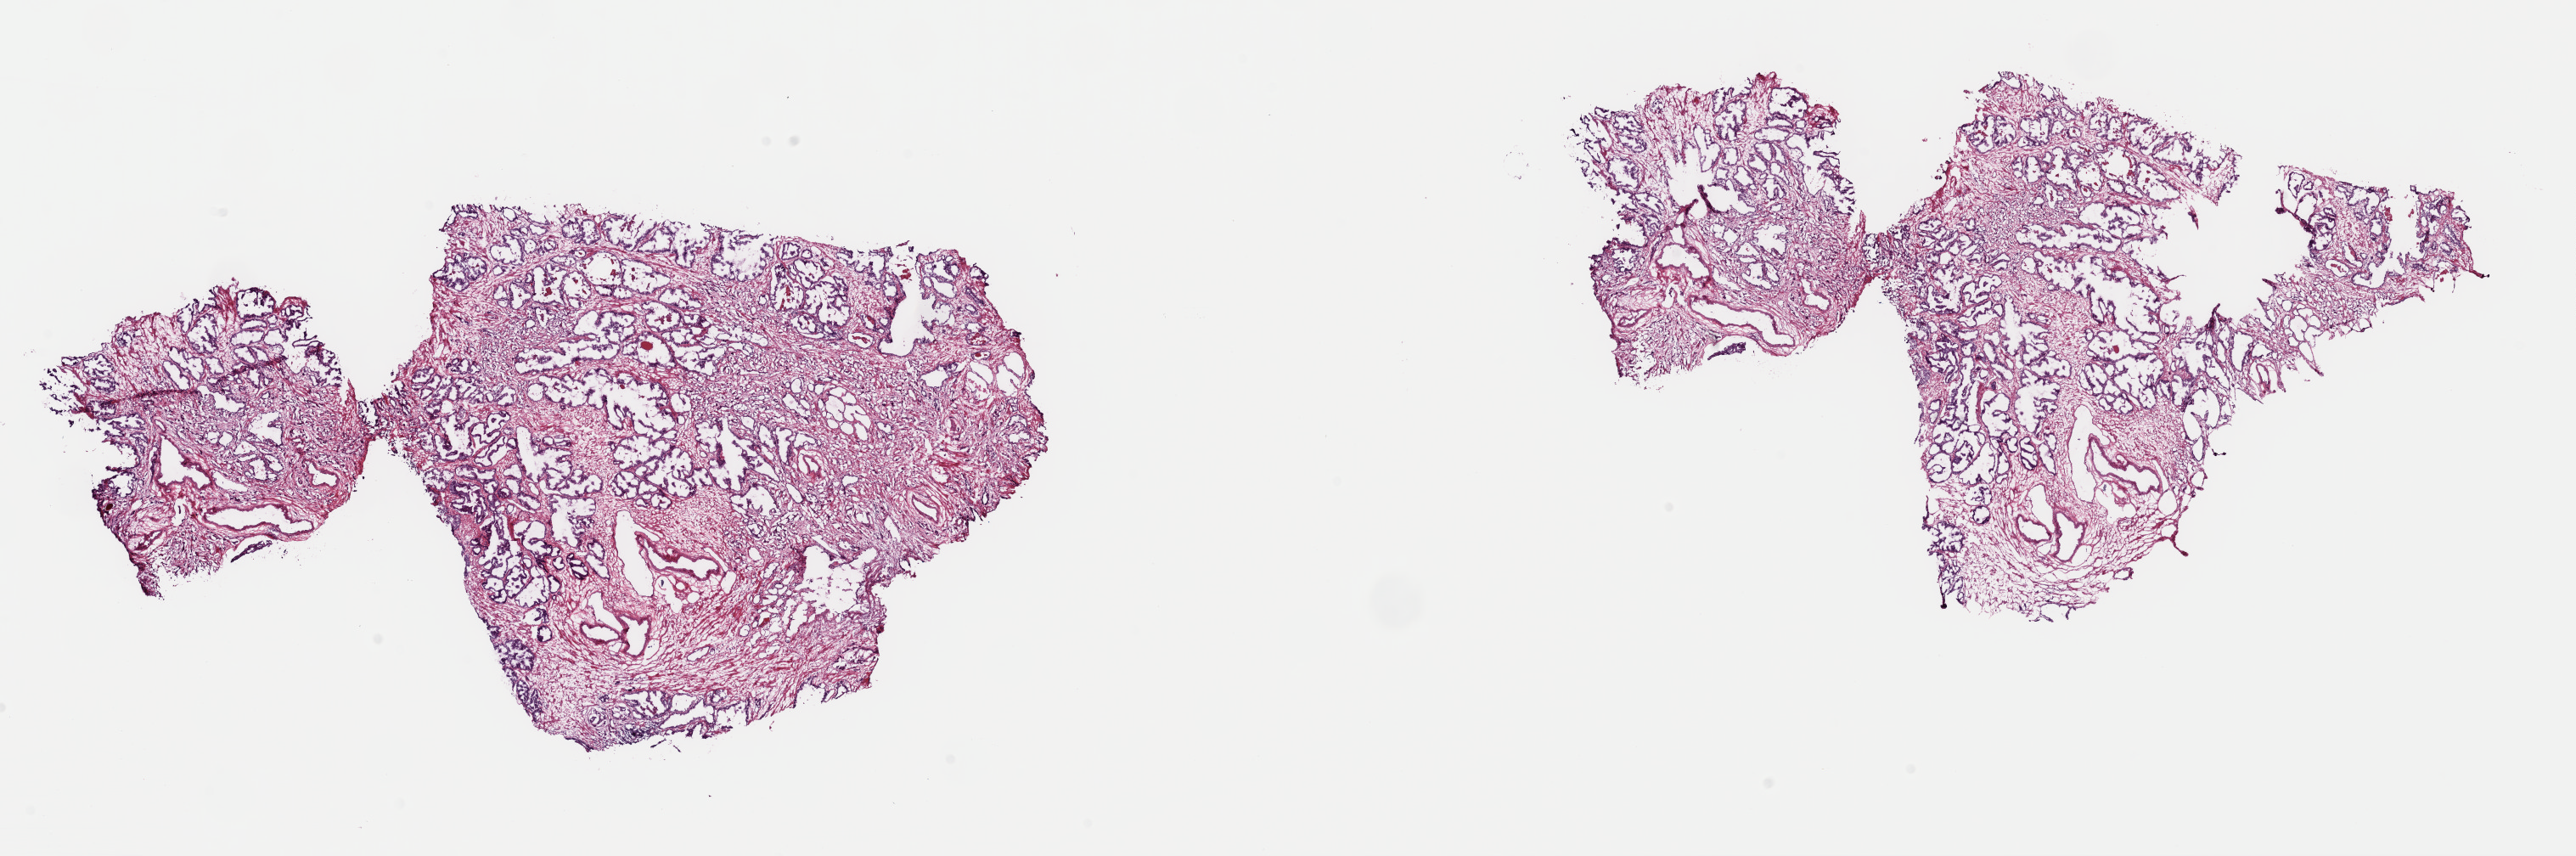
Whole-slide histology image, Hematoxylin and eosin (H&E) stained, shown as a low-resolution overview of the whole scanned area (about 24.0 x 8.0 mm); frozen section; prostate, primary tumour sample. Male, age 54 years at initial diagnosis. Gleason score: 7 (4+3). Pathologist review of this section (percent, as recorded): tumour cells 70%, tumour nuclei 70%, normal cells 5%, stromal cells 25%, necrosis 0%. Infiltration values recorded for this section: lymphocyte infiltration 40%, monocyte infiltration 20%, neutrophil infiltration 20%.
Histologic diagnosis: Adenocarcinoma, NOS (prostate gland).